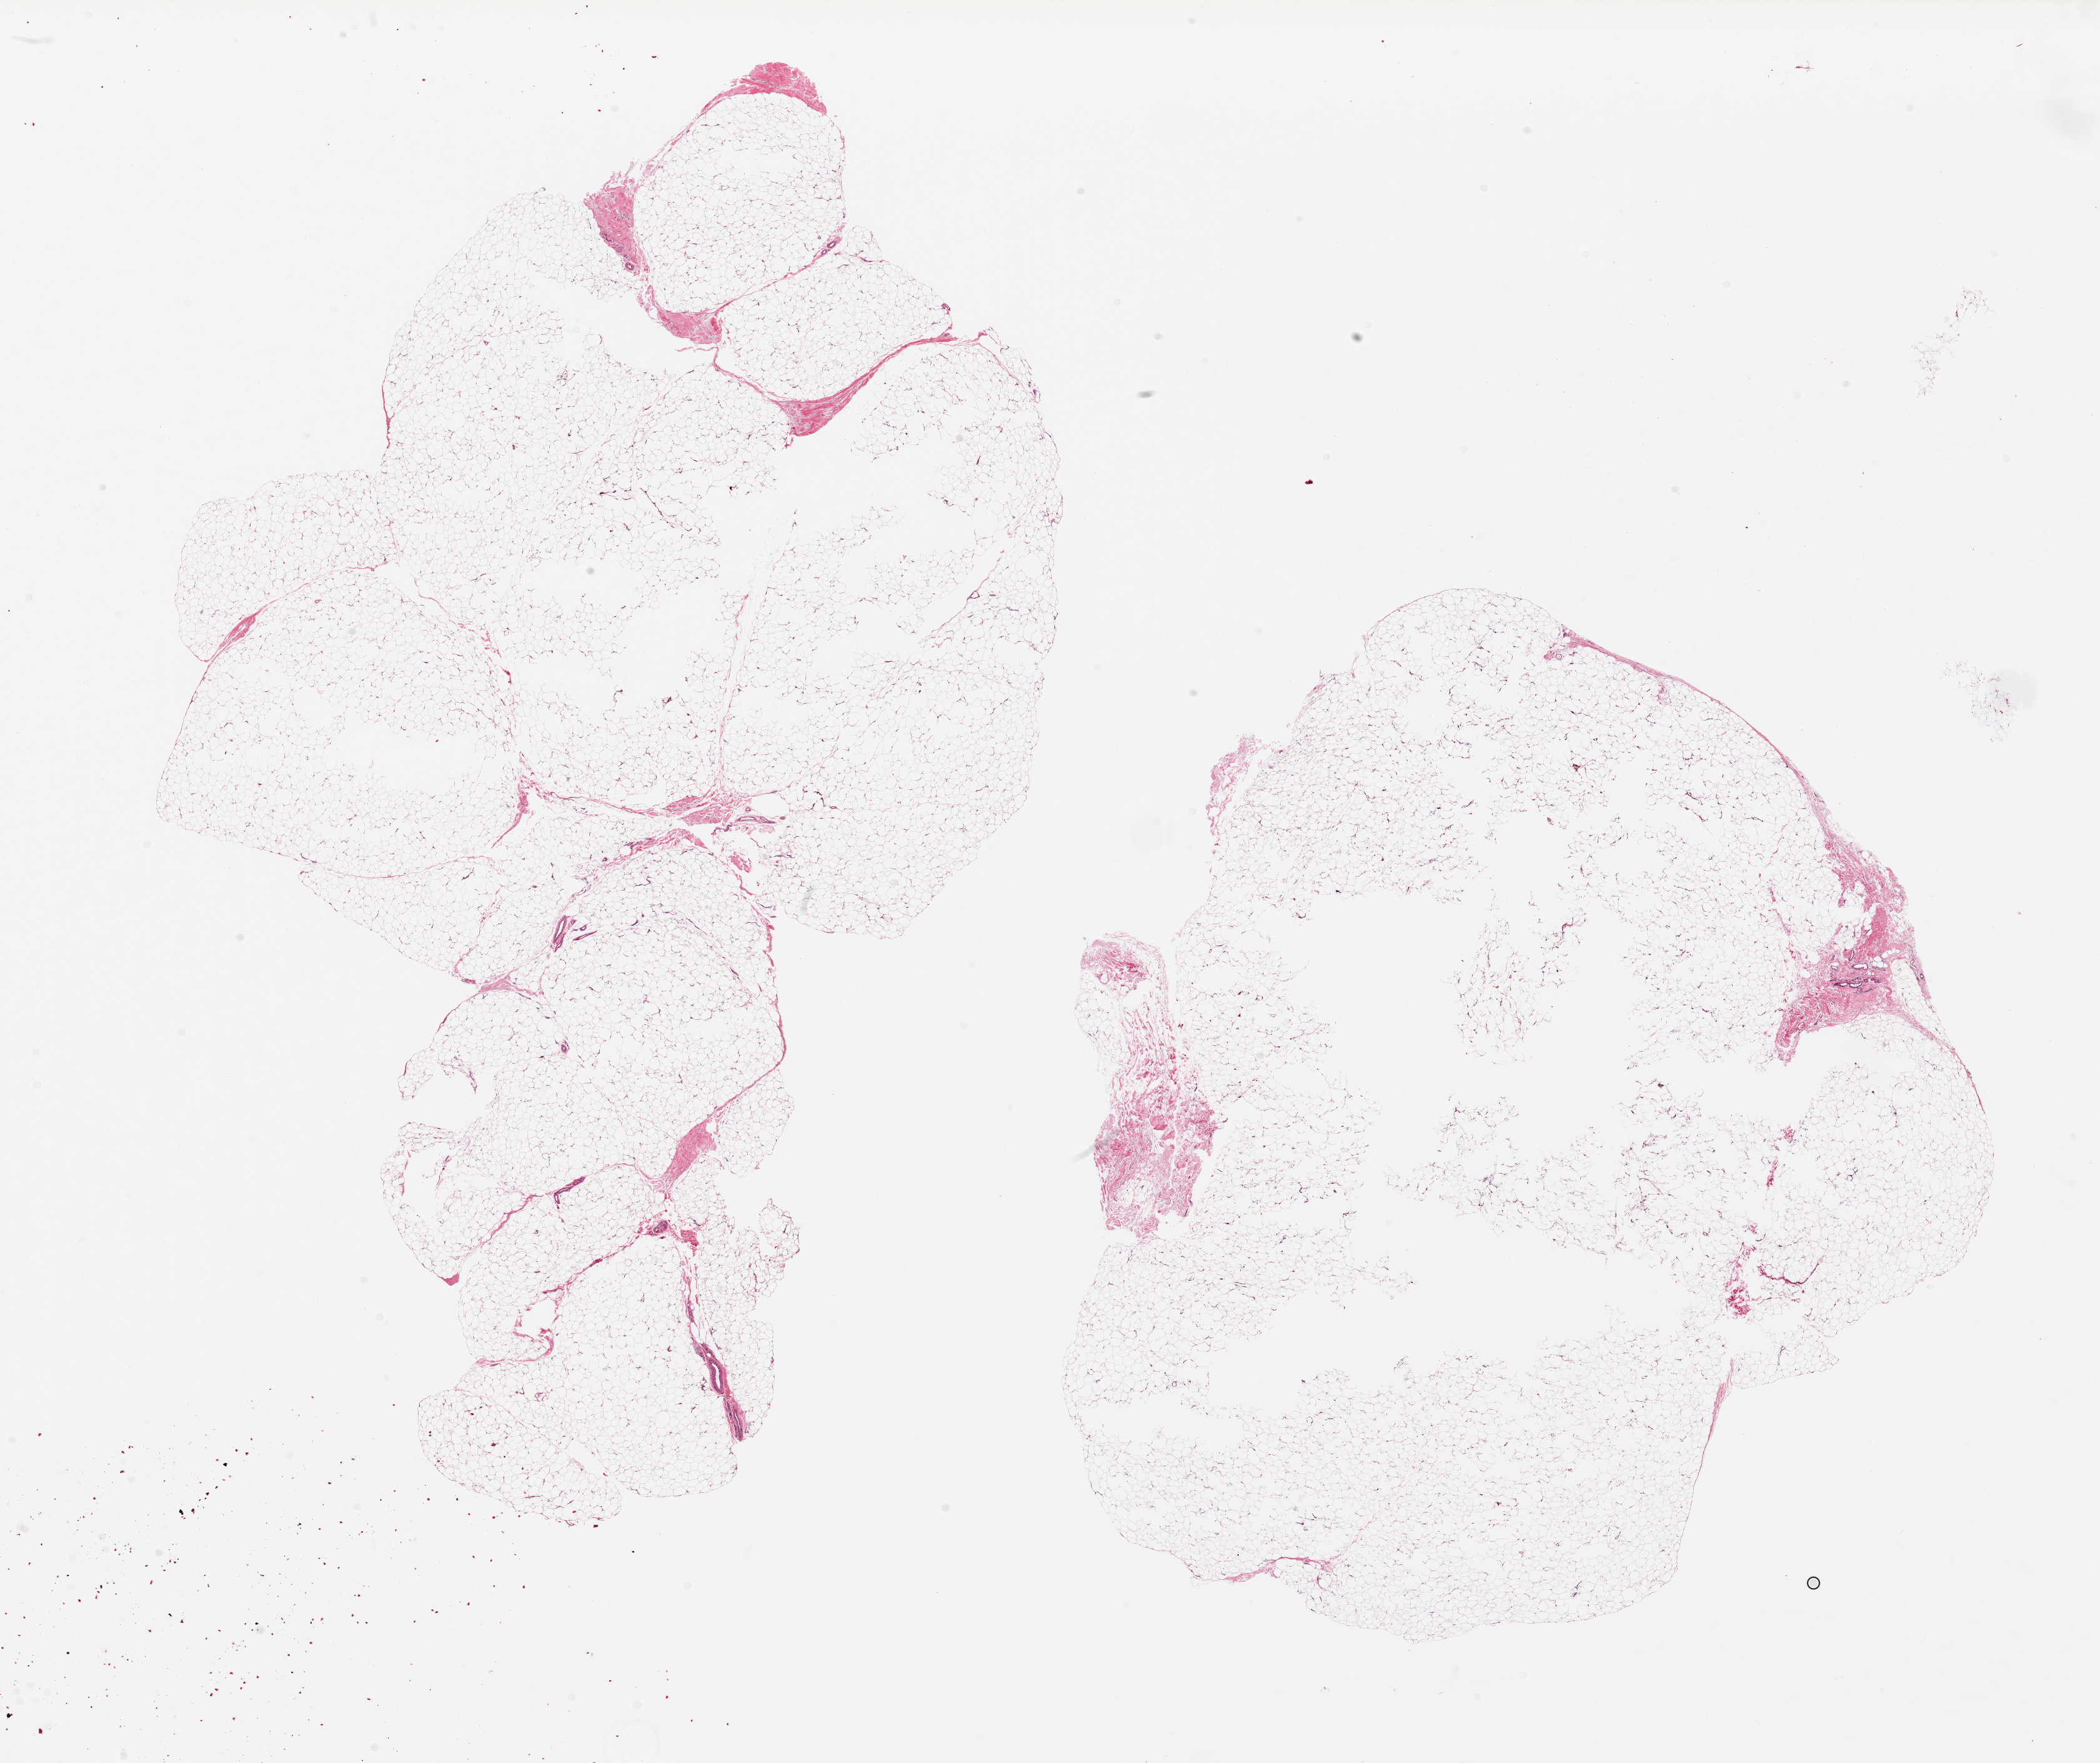
H&E whole-slide image, low-resolution overview of the scanned area, about 26.6 x 22.3 mm (slide scanned at 20x). PAXgene-fixed paraffin-embedded (PFPE) section. Target tissue: adipose tissue. Donor tissue sample.
* reviewer comment on this tissue sample: 2 pieces ~15x10mm